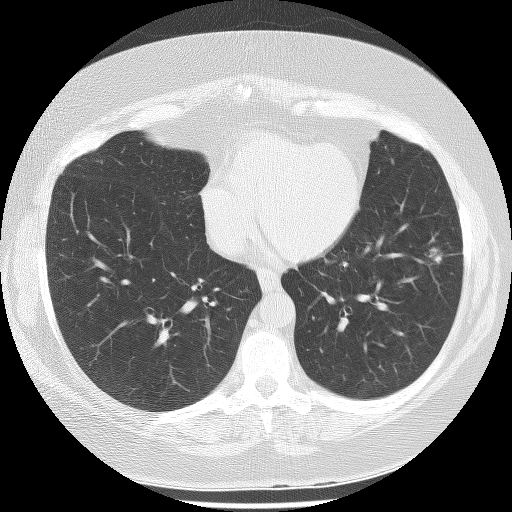
Low-dose screening chest CT, one axial slice. Slice 98 of 233 in the series (ordered by position). Reconstruction kernel BONE. 120 kVp. Lung window (W 1500 / L -600 HU). 512 × 512 image matrix, field of view 340 × 340 mm.
Outlined on this slice (manually delineated by an expert):
- lesion 1 (tumor, lower lobe of left lung): bounding box <429,248,442,264> (left, top, right, bottom; pixels)